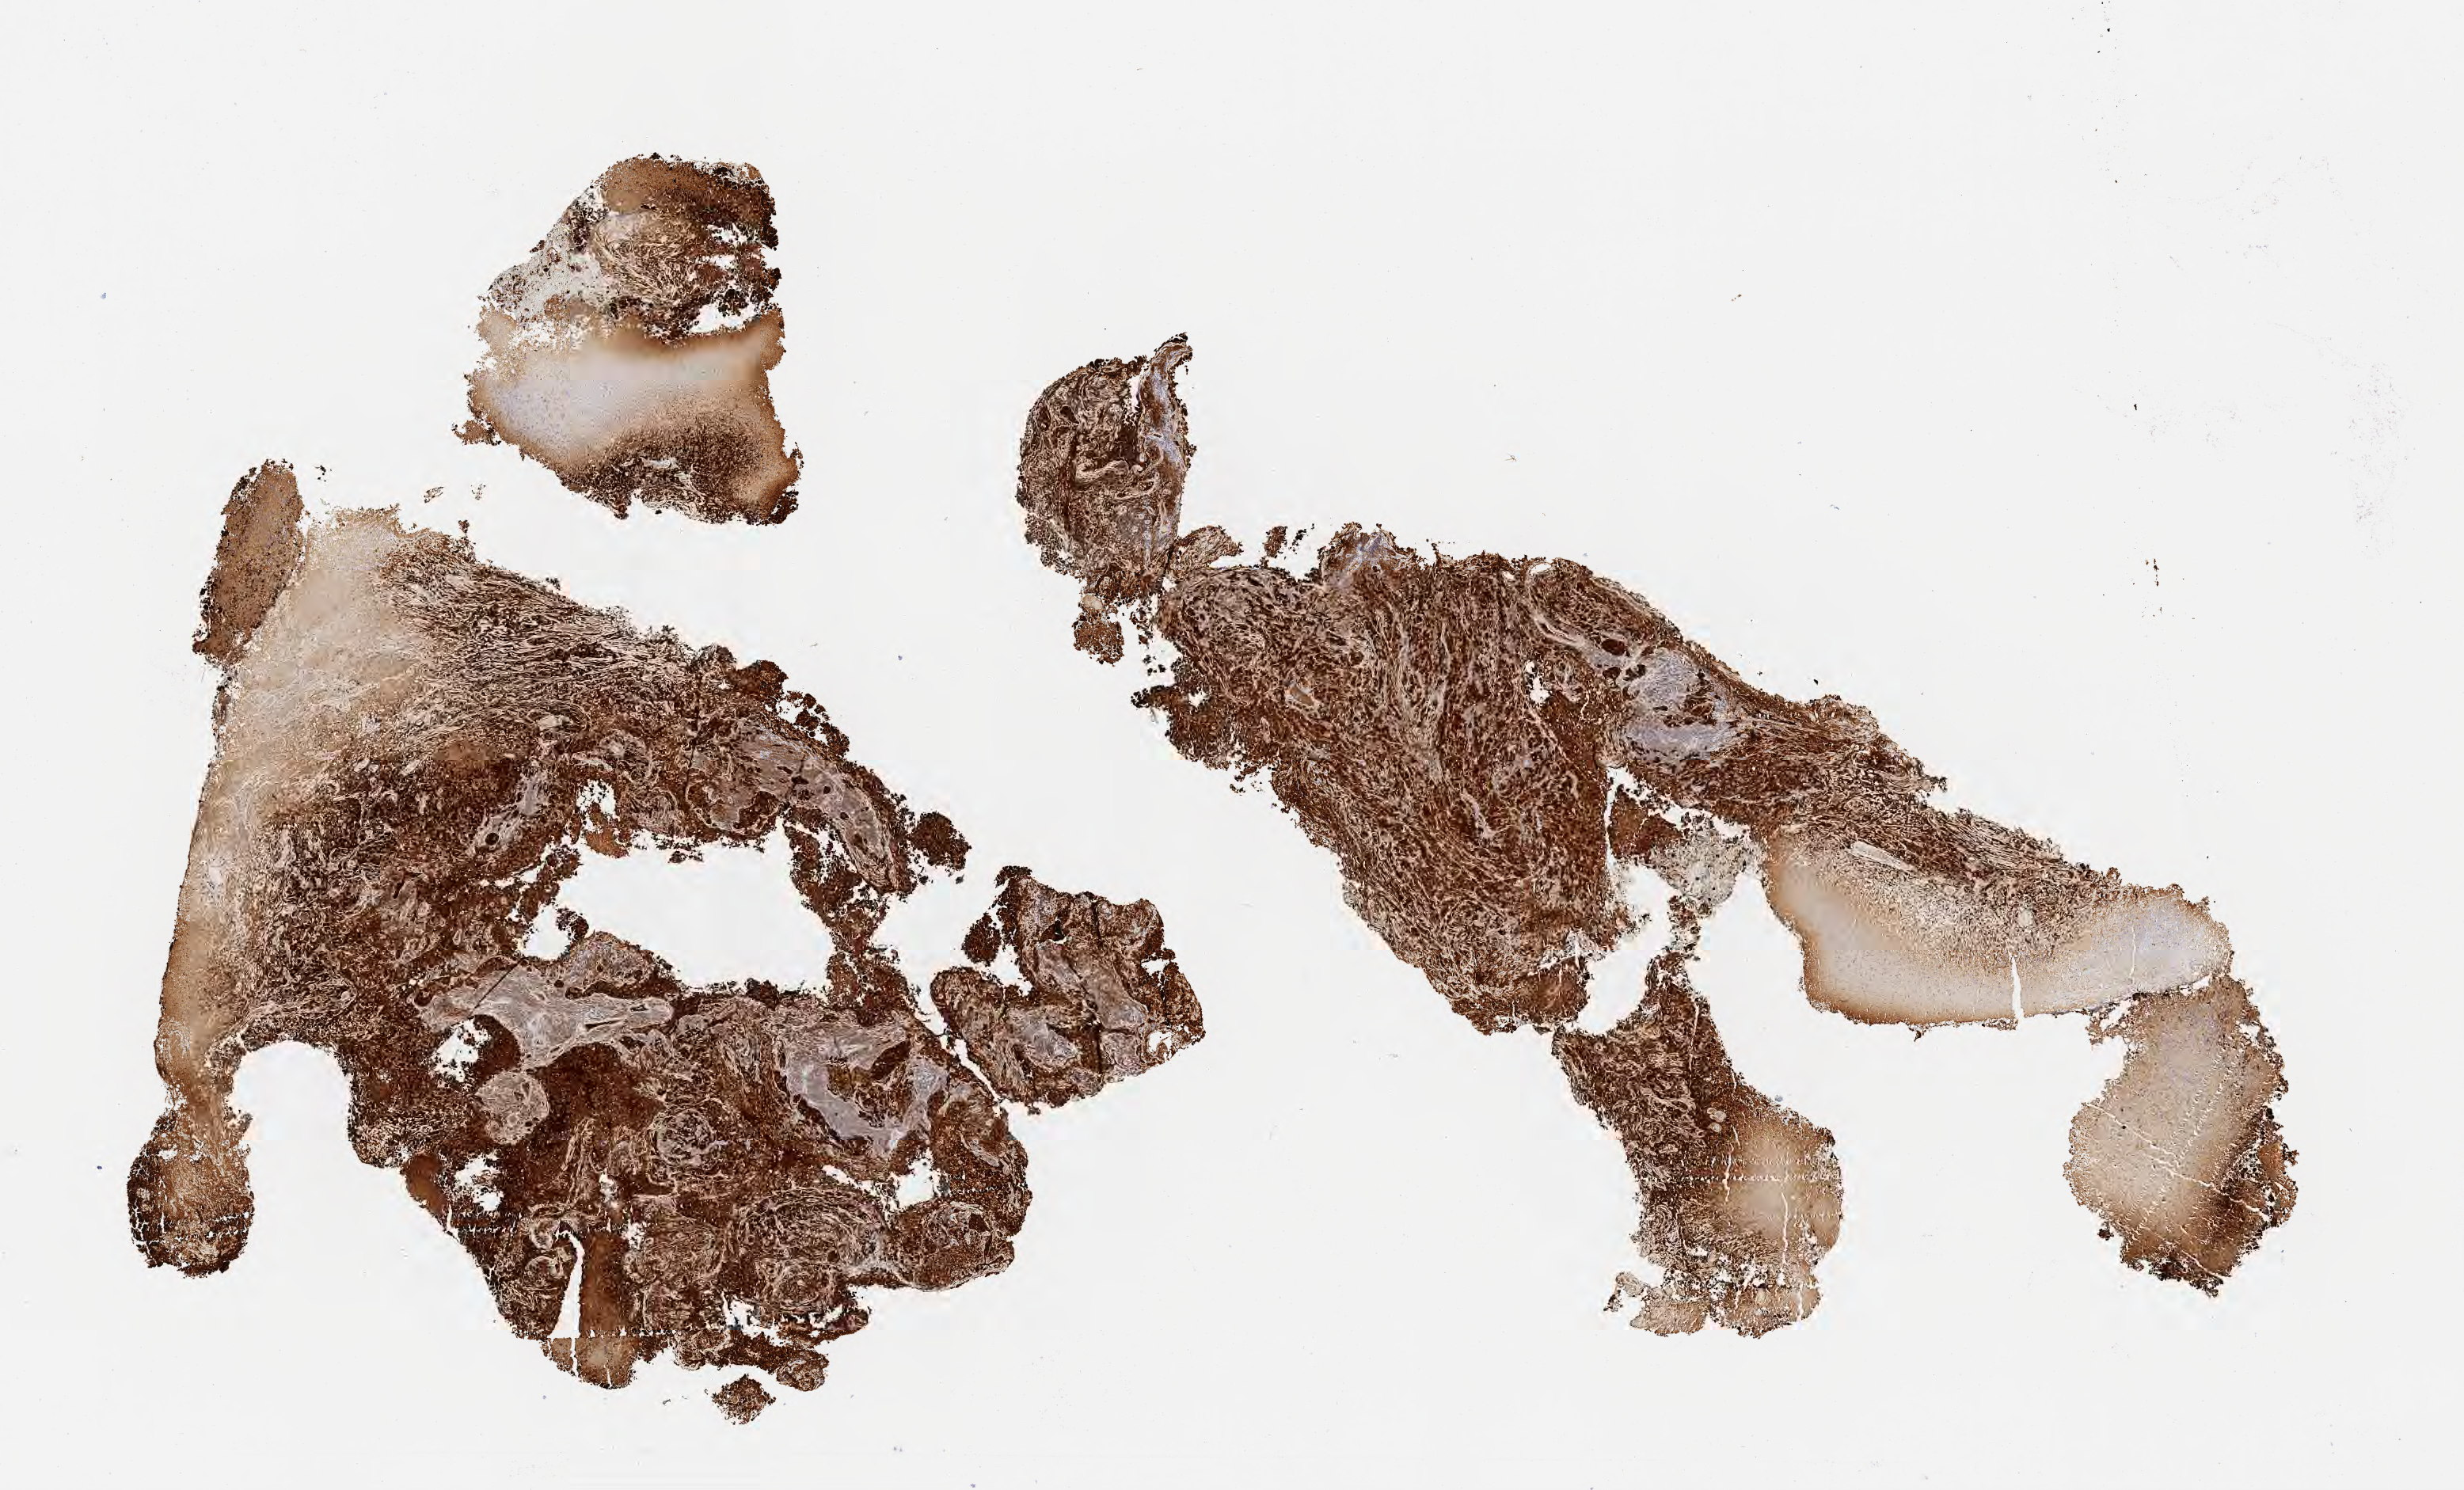
IHC for p16 (p16INK4a), whole-slide image, low-resolution overview of the scanned area, about 12.6 x 7.6 mm, specimen: tumor tissue, anatomic site: cervix. Female patient, 38 years old.
- diagnosis: Squamous cell carcinoma, large cell, nonkeratinizing, NOS